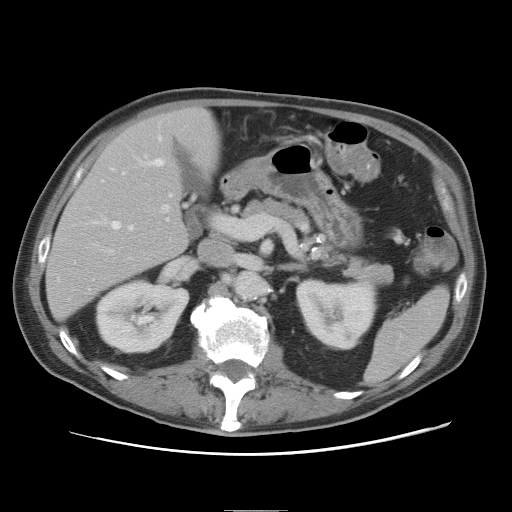
Contrast-enhanced abdominal CT, one axial slice. Slice 38 of 89 in the series (ordered by position). 120 kVp. Intravenous contrast given. Soft-tissue window (W 400 / L 40 HU). 5 mm slice thickness. 512 × 512 image matrix, field of view 375 × 375 mm. Male patient, age 69 years. From the clinical record (not read from this slice): diagnosis: colorectal cancer liver metastases, imaged before liver resection; multiple liver metastases: no; largest metastasis: 8.5 cm; disease in both lobes: no.
Structures marked on this image (outlined manually by an expert reader):
- hepatic veins: bounding box [x1, y1, x2, y2] px = [95, 136, 172, 229]
- liver: [46, 108, 219, 318]
- planned liver remnant (the part of the liver to remain after resection): [47, 108, 219, 318]
- portal vein (with intrahepatic branches): [110, 205, 224, 253]